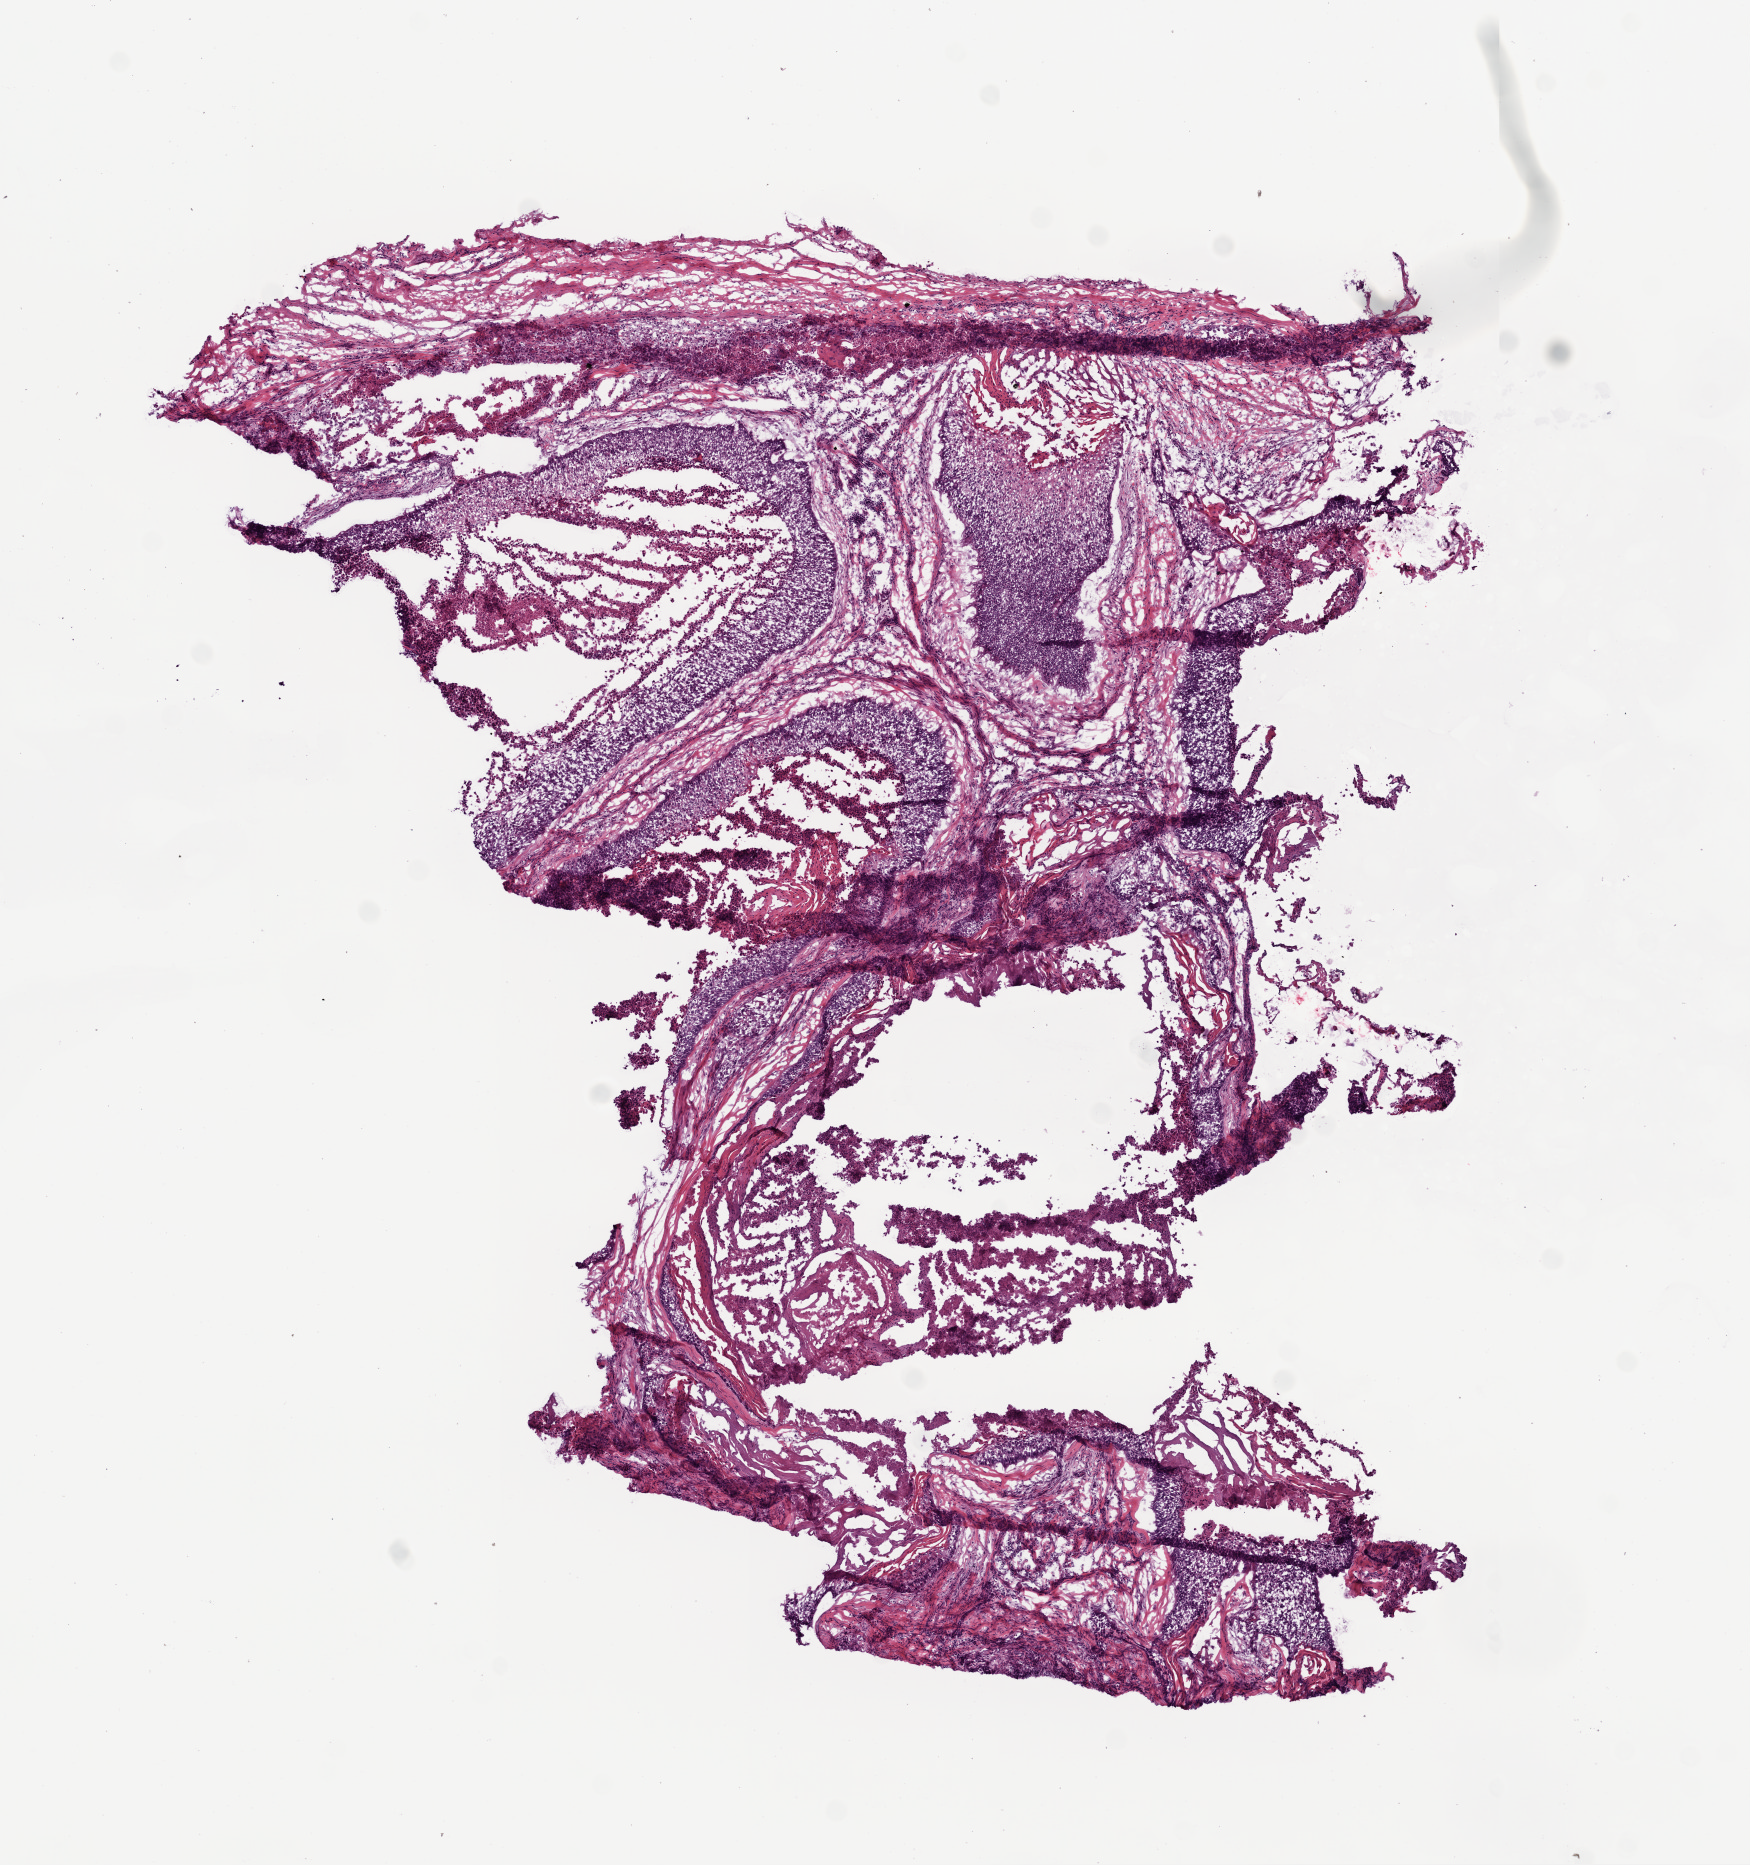
Whole-slide histology image, H&E, low-resolution overview of the scanned area, about 7.0 x 7.5 mm (from a 20x scan), frozen section from the bottom of the tissue portion, head and neck, primary tumour sample. Patient: male, age at initial diagnosis 60 years. Histologic grade: G2 (moderately differentiated). Slide review estimates, as recorded: tumour cells 50%, tumour nuclei 70%, normal cells 0%, stromal cells 40%, necrosis 10%.
• TNM: T4a N2b
• diagnosis: Squamous cell carcinoma, NOS
• AJCC pathologic stage: IVA
• lymph nodes positive (case pathology): 7 of 30 examined